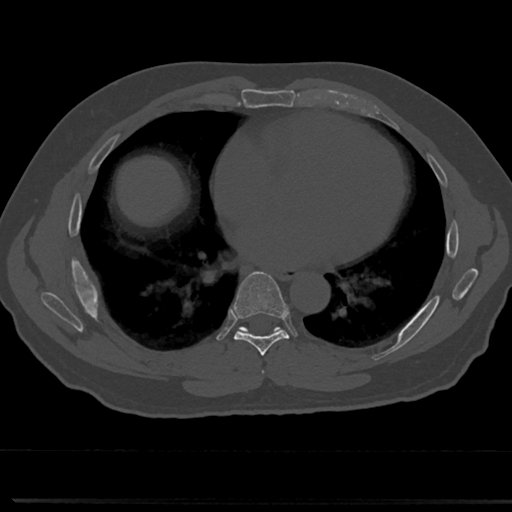
CT including the spine, one axial slice. Position 396 of 817 along the scan axis. Bone window (W 1800 / L 400 HU). 512 × 512 image matrix. Patient: male, 61 years. Case-level facts recorded for this patient, not image findings: primary cancer: prostate.
Outlined on this slice (semi-automatically segmented with operator editing):
- T6 vertebra: bounding box <261,340,319,377> (left, top, right, bottom; pixels)
- T7 vertebra: <214,275,310,358>